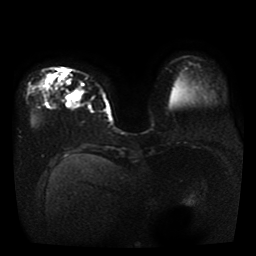
Breast MRI, one axial slice; position 13 of 41 along the scan axis; diffusion-weighted series; image 2 of 4 stored at this slice position (different b-values; order by instance number); 1.5 T; 5 mm slice thickness; 256 × 256 image matrix, field of view 330 × 330 mm. Female patient.
Annotated regions visible in this slice (outlined manually by an expert reader):
- tumour on diffusion-weighted imaging: bounding box [x1, y1, x2, y2] px = [71, 91, 79, 100]